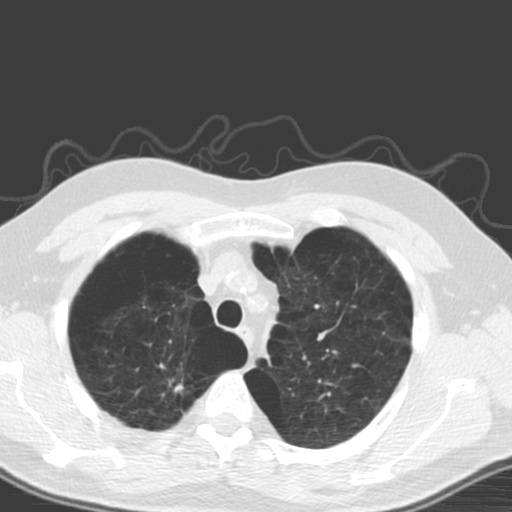
Low-dose screening chest CT, one axial slice; slice 138 of 173 in the series (ordered by position); 120 kVp; lung window (W 1500 / L -600 HU); 3.2 mm slice thickness; 512 × 512 image matrix, field of view 340 × 340 mm.
Structures marked on this image (expert manual segmentation):
- lesion 1 (tumor, upper lobe of right lung): bounding box (x1, y1, x2, y2) in pixels: (174, 384, 184, 393)